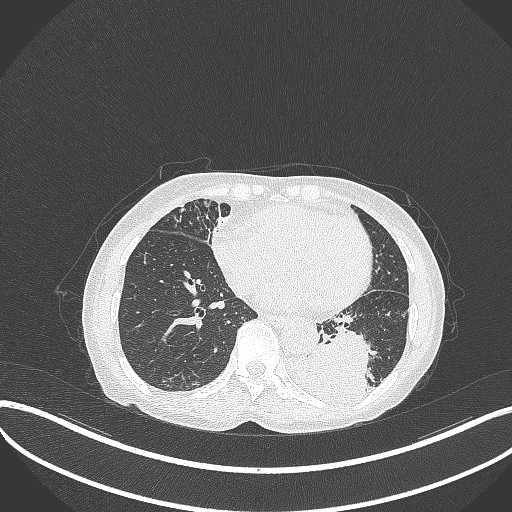
Chest CT, one axial slice; position 105 of 370 along the scan axis; lung window (W 1500 / L -600 HU); 512 × 512 image matrix. Patient: female, 78 years. From the clinical record (not read from this slice): clinical TNM (as recorded): T3 N0 M1.
Structures marked on this image (rectangle marked by the reading radiologist):
- lung tumour (recorded histology: squamous cell carcinoma): box from (x=283, y=332) to (x=372, y=409) px